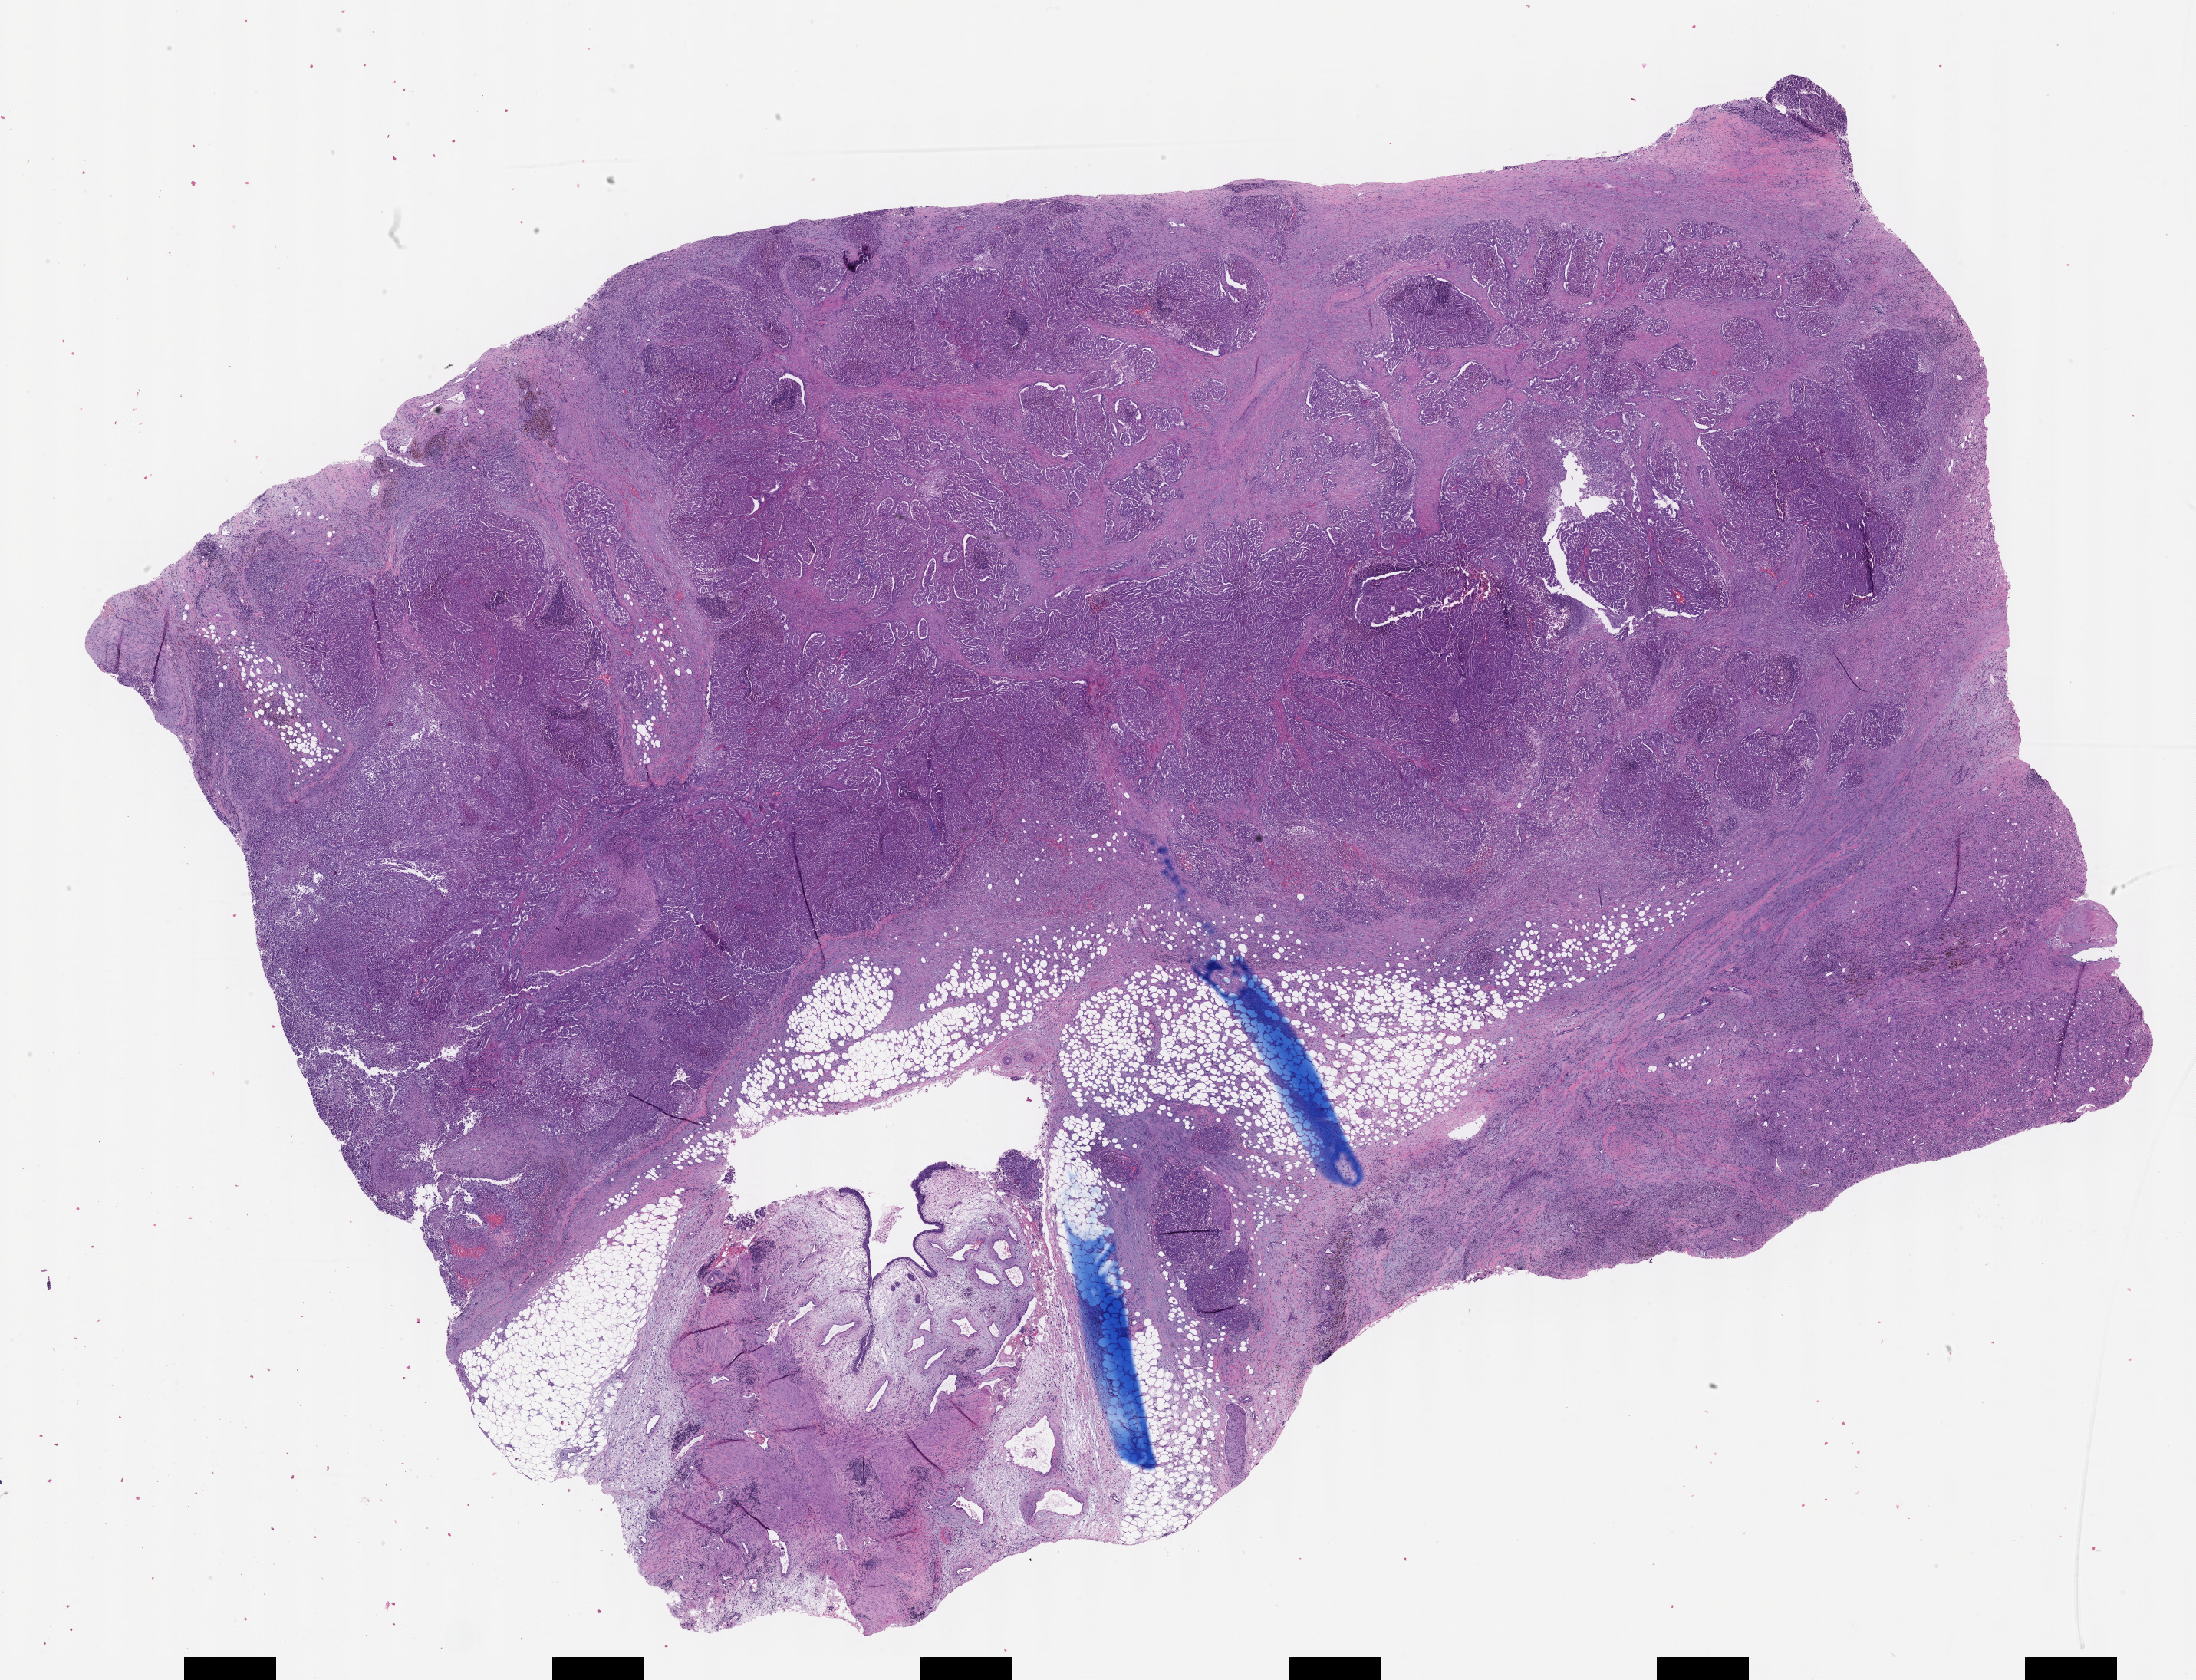
Digitized H&E tissue section (whole slide), whole scanned area (about 23.1 x 17.7 mm, from a 40x scan) shown as a low-resolution overview, formalin-fixed paraffin-embedded (FFPE) diagnostic section, primary tumour sample from the kidney. Male, age 85 years at initial diagnosis.
• pathologic diagnosis: Papillary adenocarcinoma, NOS
• TNM: T3b N0 MX
• laterality: left
• AJCC pathologic stage: III (7th edition)